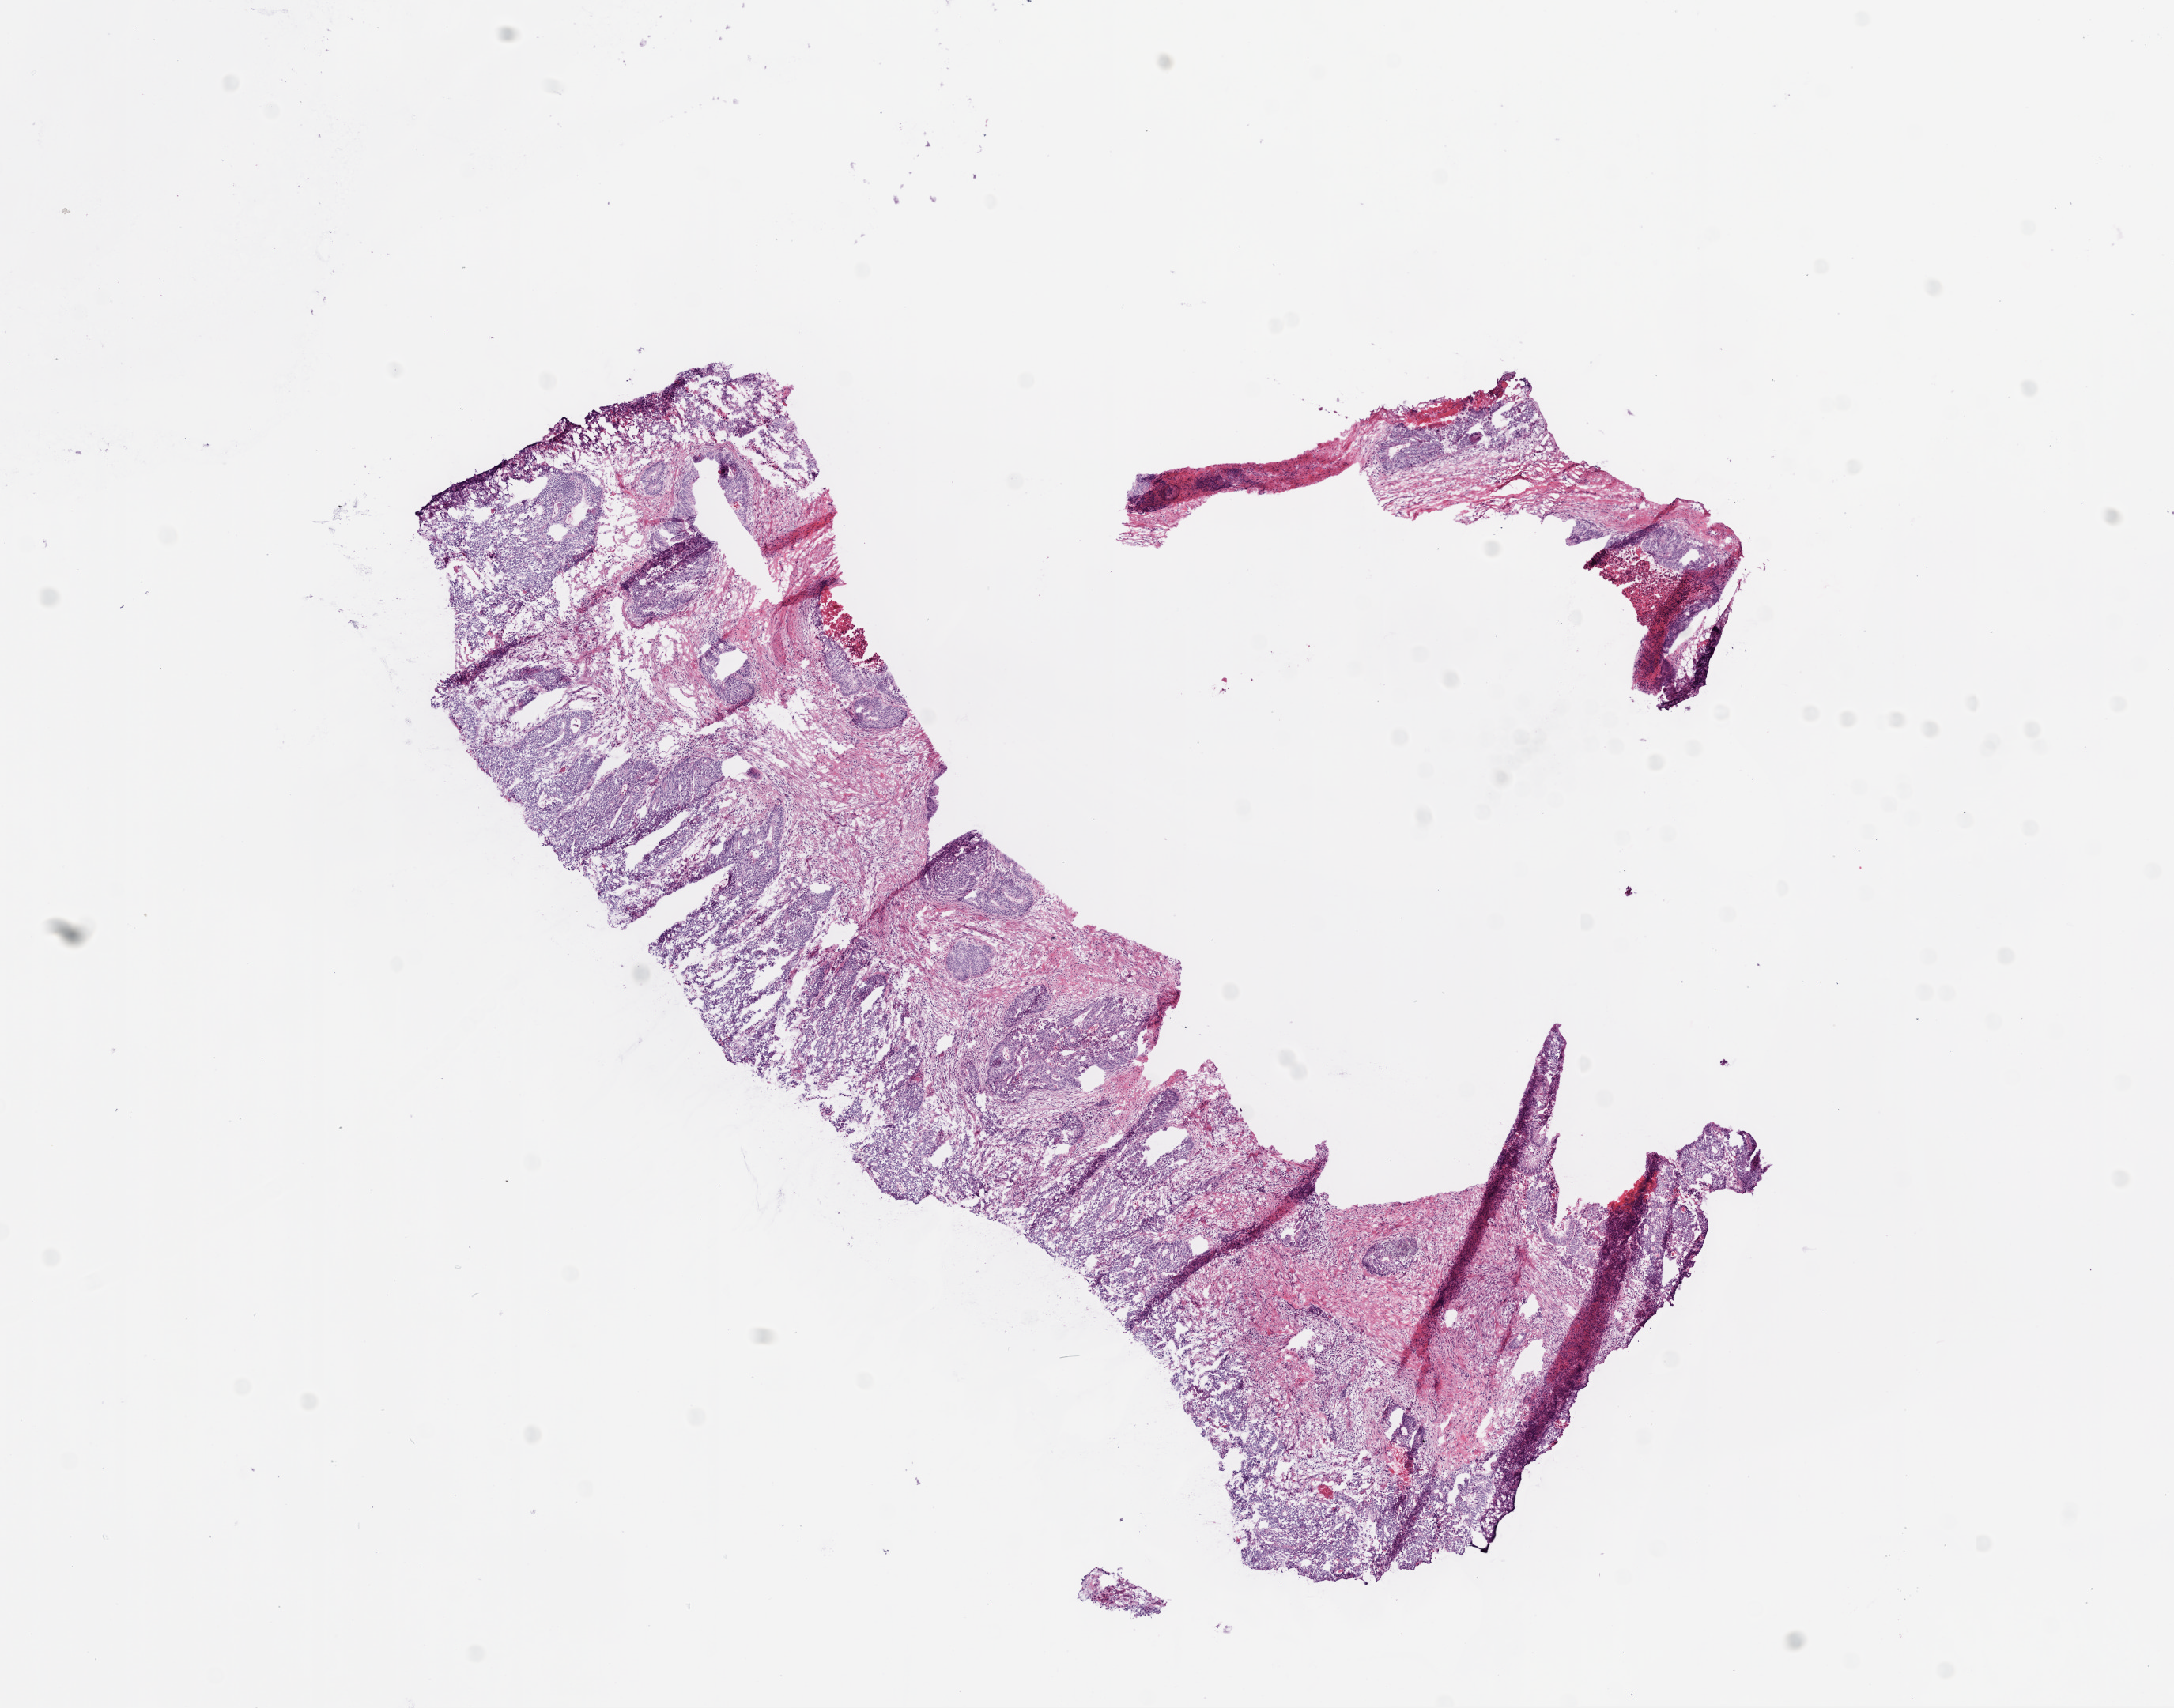
Whole-slide histology image, H&E-stained, whole scanned area (about 11.0 x 8.7 mm, acquisition: 20x scan) shown as a low-resolution overview; frozen section from the bottom of the tissue portion; sample: primary tumour, colon. Patient: female, age at initial diagnosis 81 years. Composition of this section per pathologist review: tumour cells 80%, tumour nuclei 80%, normal cells 0%, stromal cells 20%, necrosis 0%.
AJCC pathologic stage: I (6th edition). TNM: T2 N0 M0. Lymph nodes positive (case pathology): 0 of 12 examined. Histologic diagnosis: Adenocarcinoma, NOS.